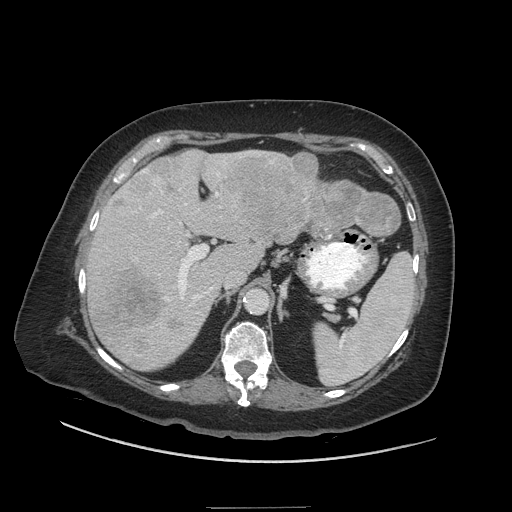
Contrast-enhanced abdominal CT (liver protocol), one axial slice; slice 29 of 81 in the series (ordered by position); 140 kVp; soft-tissue window (W 400 / L 40 HU); 2.5 mm slice thickness; 512 × 512 image matrix, field of view 440 × 440 mm. Case-level facts recorded for this patient, not image findings: diagnosis: hepatocellular carcinoma (patient treated with transarterial chemoembolisation; whether this scan precedes or follows treatment is not stated here); TNM stage (as recorded): Stage-II; Child-Pugh class: A; tumour differentiation: moderately differentiated; tumour size: 1.7 cm.
Outlined on this slice (semi-automatically segmented with operator editing):
- liver parenchyma outside the tumour (the mass and vessels are separate outlines, so this box may not span the whole liver): box from (x=86, y=150) to (x=346, y=370) px
- mass: (x=93, y=152)–(x=401, y=353)
- liver vessels: (x=122, y=152)–(x=255, y=356)